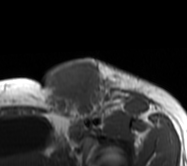
MRI of an extremity soft-tissue mass, one axial slice; slice 43 of 62 in the series (ordered by position); MR volume resampled by the dataset authors to the PET/CT grid (not the native acquisition matrix); 187 × 166 image matrix. Female patient. Case-level facts recorded for this patient, not image findings: histological type: leiomyosarcoma; grade: high; site of the primary tumour: groin.
Annotated regions visible in this slice (expert contour drawn on MRI and transferred to this co-registered scan by the dataset authors):
- gross tumour volume including surrounding oedema: bounding box <43,58,152,130> (left, top, right, bottom; pixels)
- gross tumour volume (mass): <43,60,110,118>